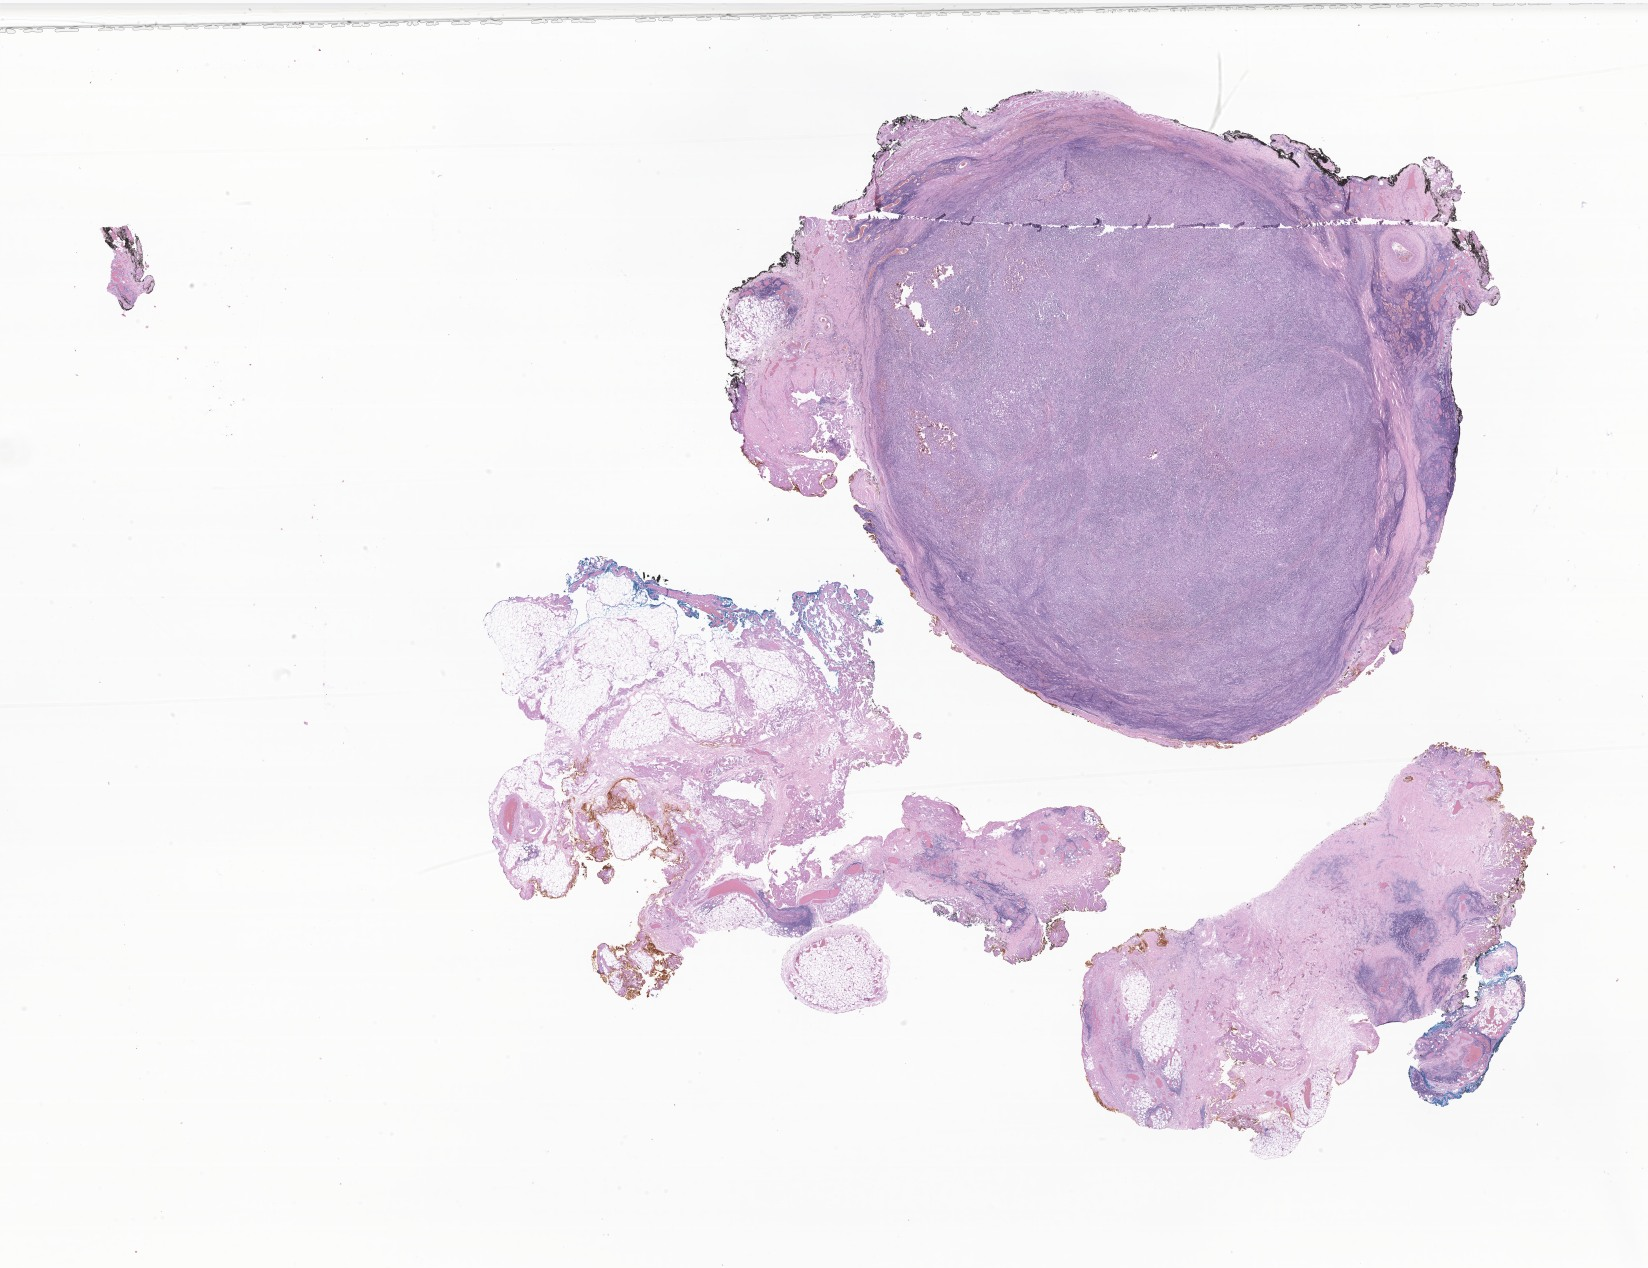
Haematoxylin and eosin whole-slide image of tumor tissue from the soft tissue, low-resolution overview of the scanned area, about 27.8 x 21.4 mm; formalin-fixed paraffin-embedded section. Patient: male, age 77 months (6 years 5 months).
Diagnosis (ICD-O-3 morphology term): Angiomatoid fibrous histiocytoma.